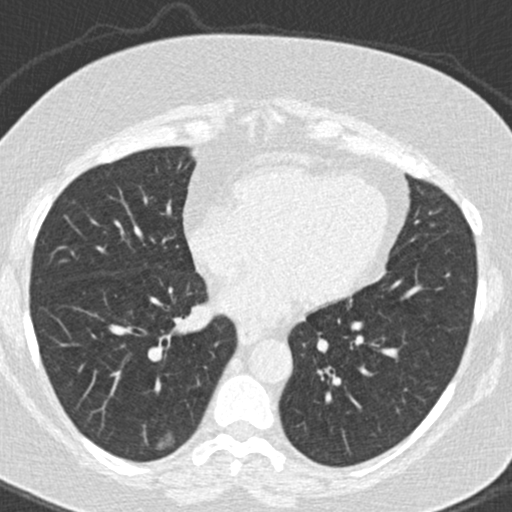
Low-dose screening chest CT, one axial slice; position 69 of 177 along the scan axis; lung window (W 1500 / L -600 HU); 2 mm slice thickness; 512 × 512 image matrix, field of view 300 × 300 mm.
Annotated regions visible in this slice (expert manual segmentation):
- lesion 1 (tumor, lower lobe of right lung): bounding box <156,433,175,449> (left, top, right, bottom; pixels)